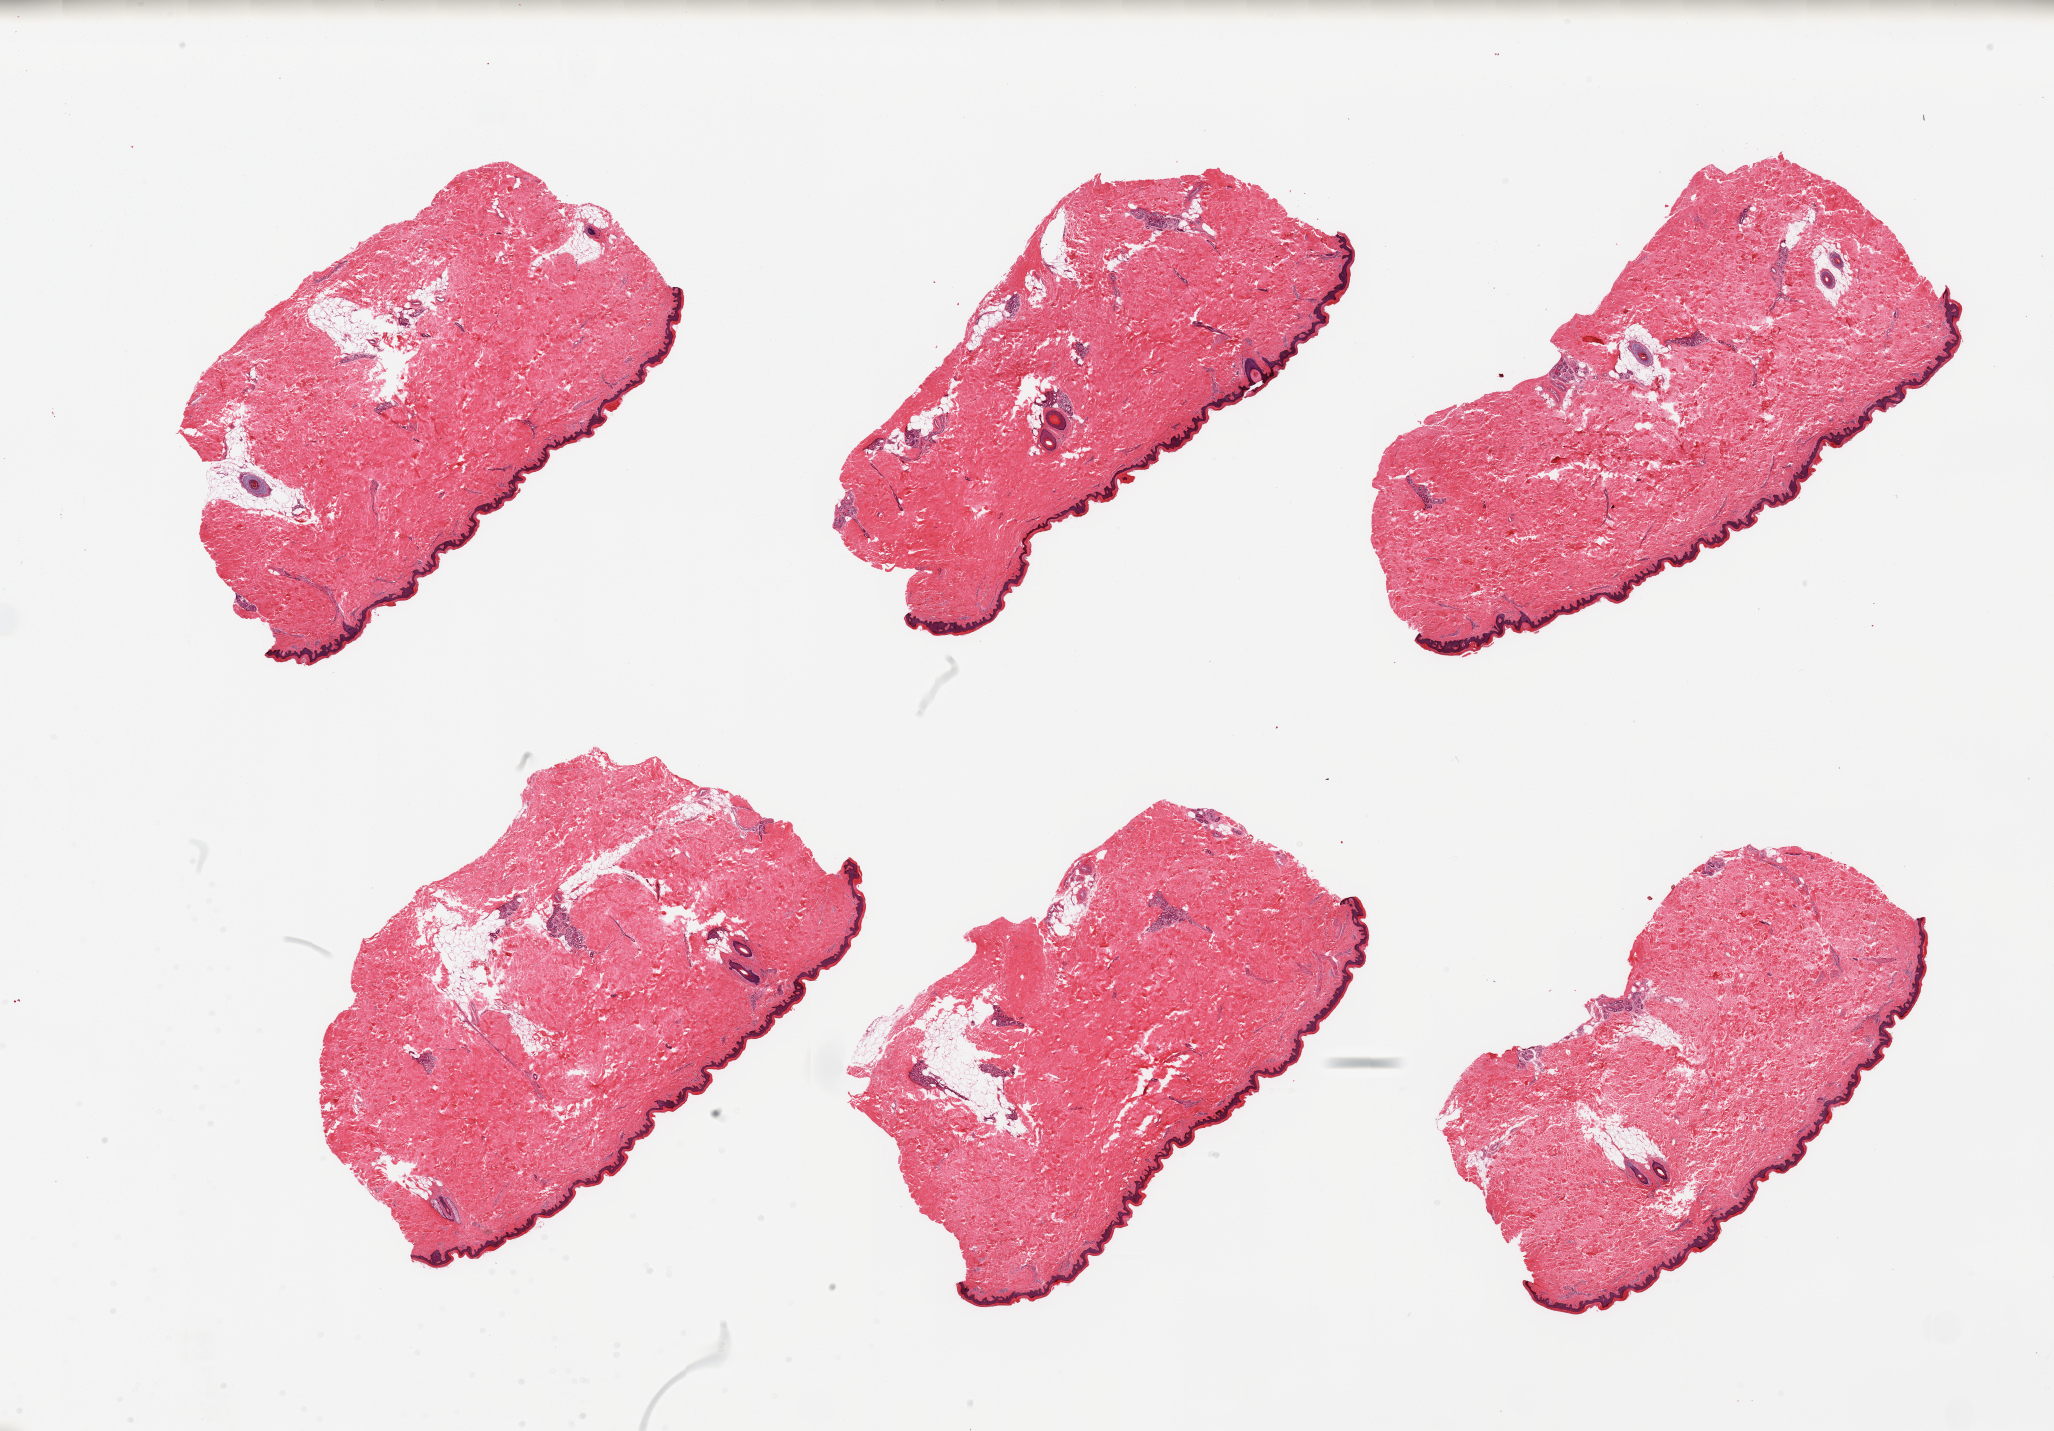
Whole-slide image, haematoxylin and eosin stain — whole scanned area (about 32.5 x 22.6 mm, acquisition: 20x scan) shown as a low-resolution overview; PAXgene-fixed paraffin-embedded (PFPE) section; target tissue: skin of lower leg; tissue donor sample.
Reviewer comment on this tissue sample: 6 pieces; well trimmed, but with 10% intradermal fat.